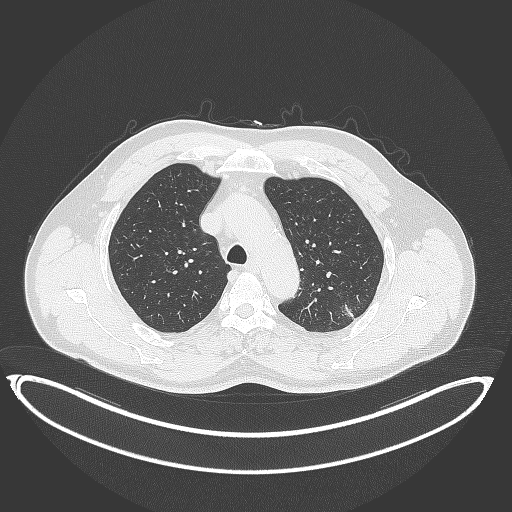
Chest CT, one axial slice; position 275 of 399 along the scan axis; reconstruction kernel B70f; lung window (W 1500 / L -600 HU); 1 mm slice thickness; 512 × 512 image matrix. Patient: male, 58 years. From the clinical record (not read from this slice): clinical TNM (as recorded): T1c N0 M0; histopathological grade: G1-2.
Outlined on this slice (bounding box drawn by a radiologist):
- lung tumour (recorded histology: adenocarcinoma): bounding box <337,302,358,326> (left, top, right, bottom; pixels)